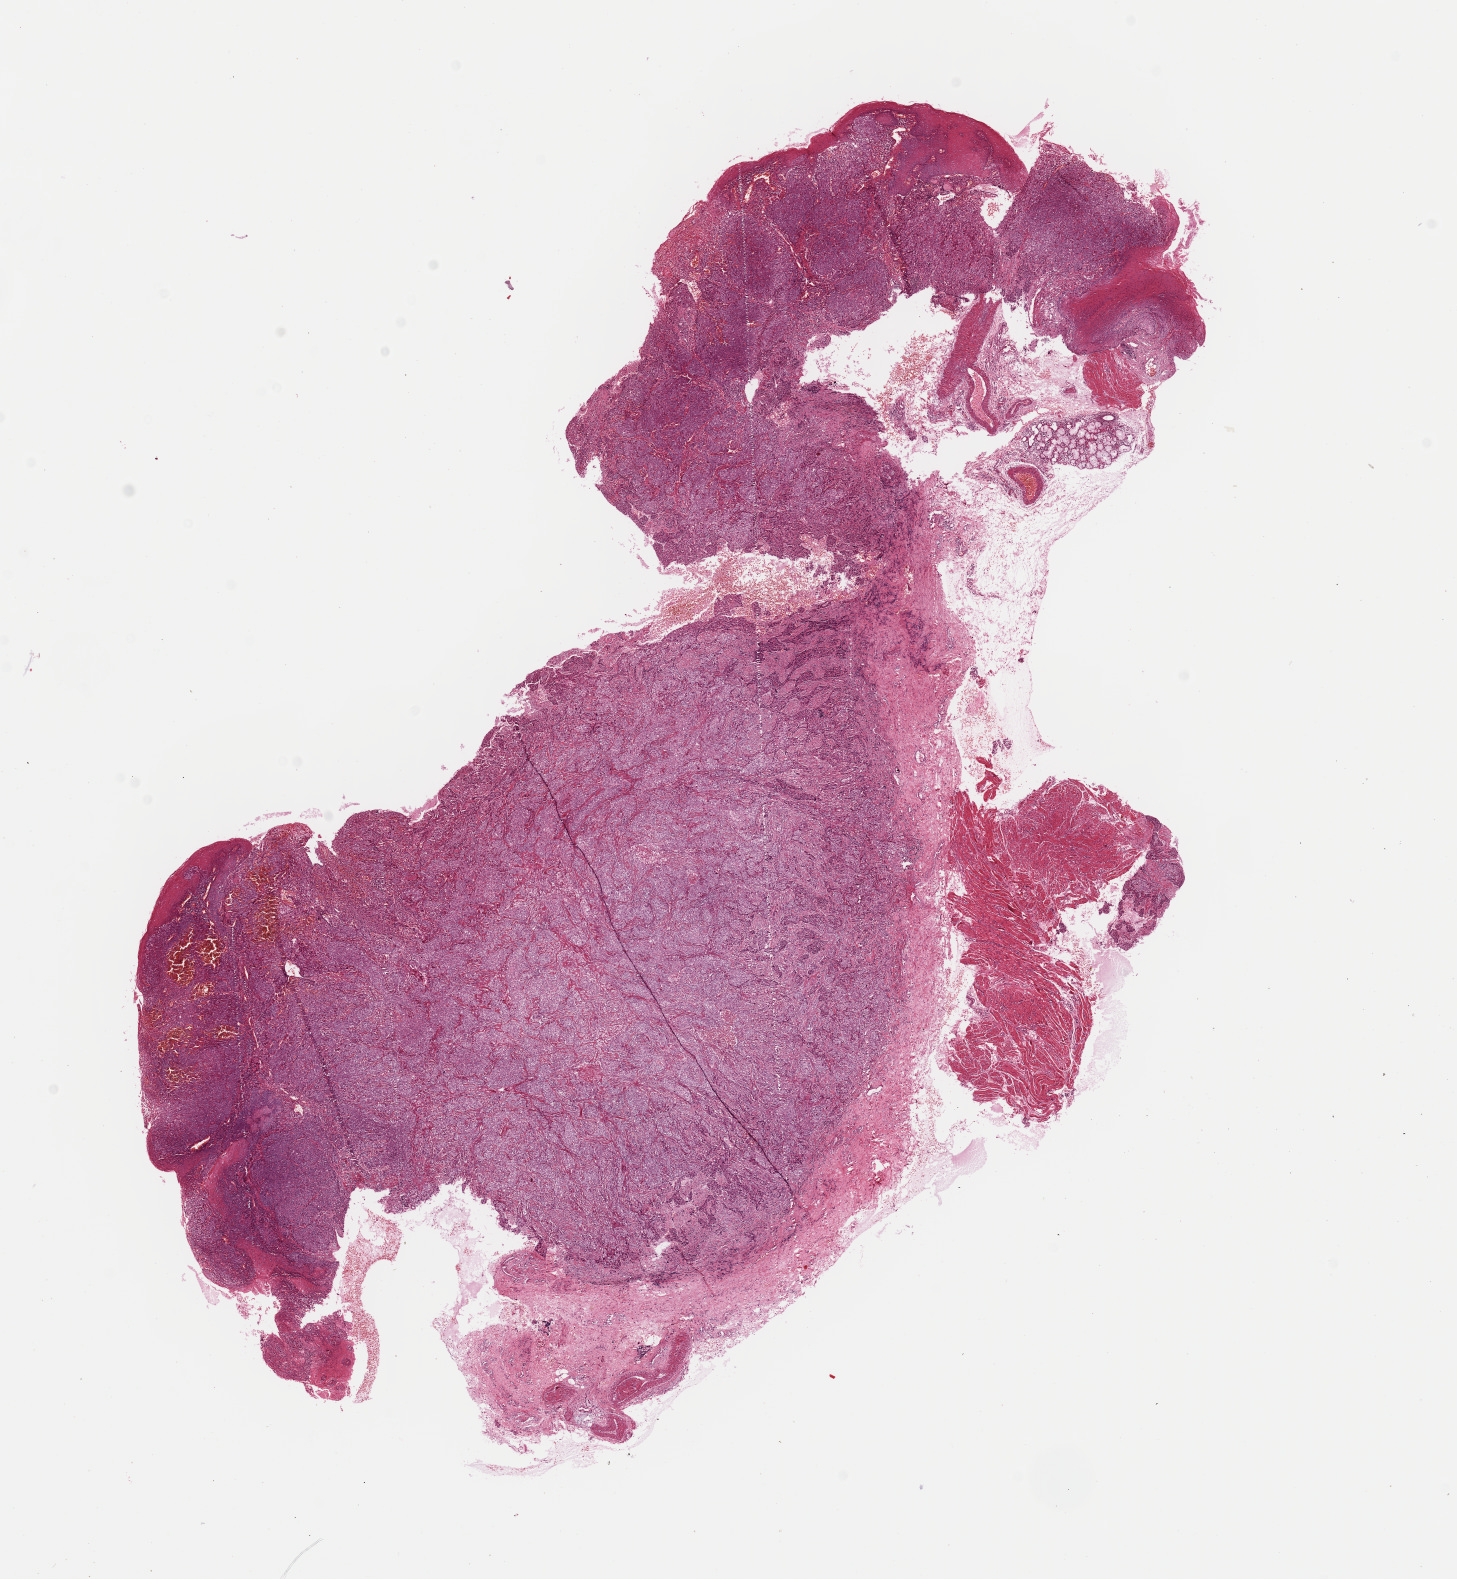
H&E whole-slide image — low-resolution overview of the scanned area, about 11.5 x 12.5 mm (acquisition: 40x scan). Formalin-fixed paraffin-embedded (FFPE) diagnostic section. Sample: primary tumour, esophagus. Male patient; age at initial diagnosis 52 years. Histologic grade: G2 (moderately differentiated).
Histologic diagnosis: Squamous cell carcinoma, NOS (middle third of esophagus). AJCC pathologic stage: IIA (6th edition).